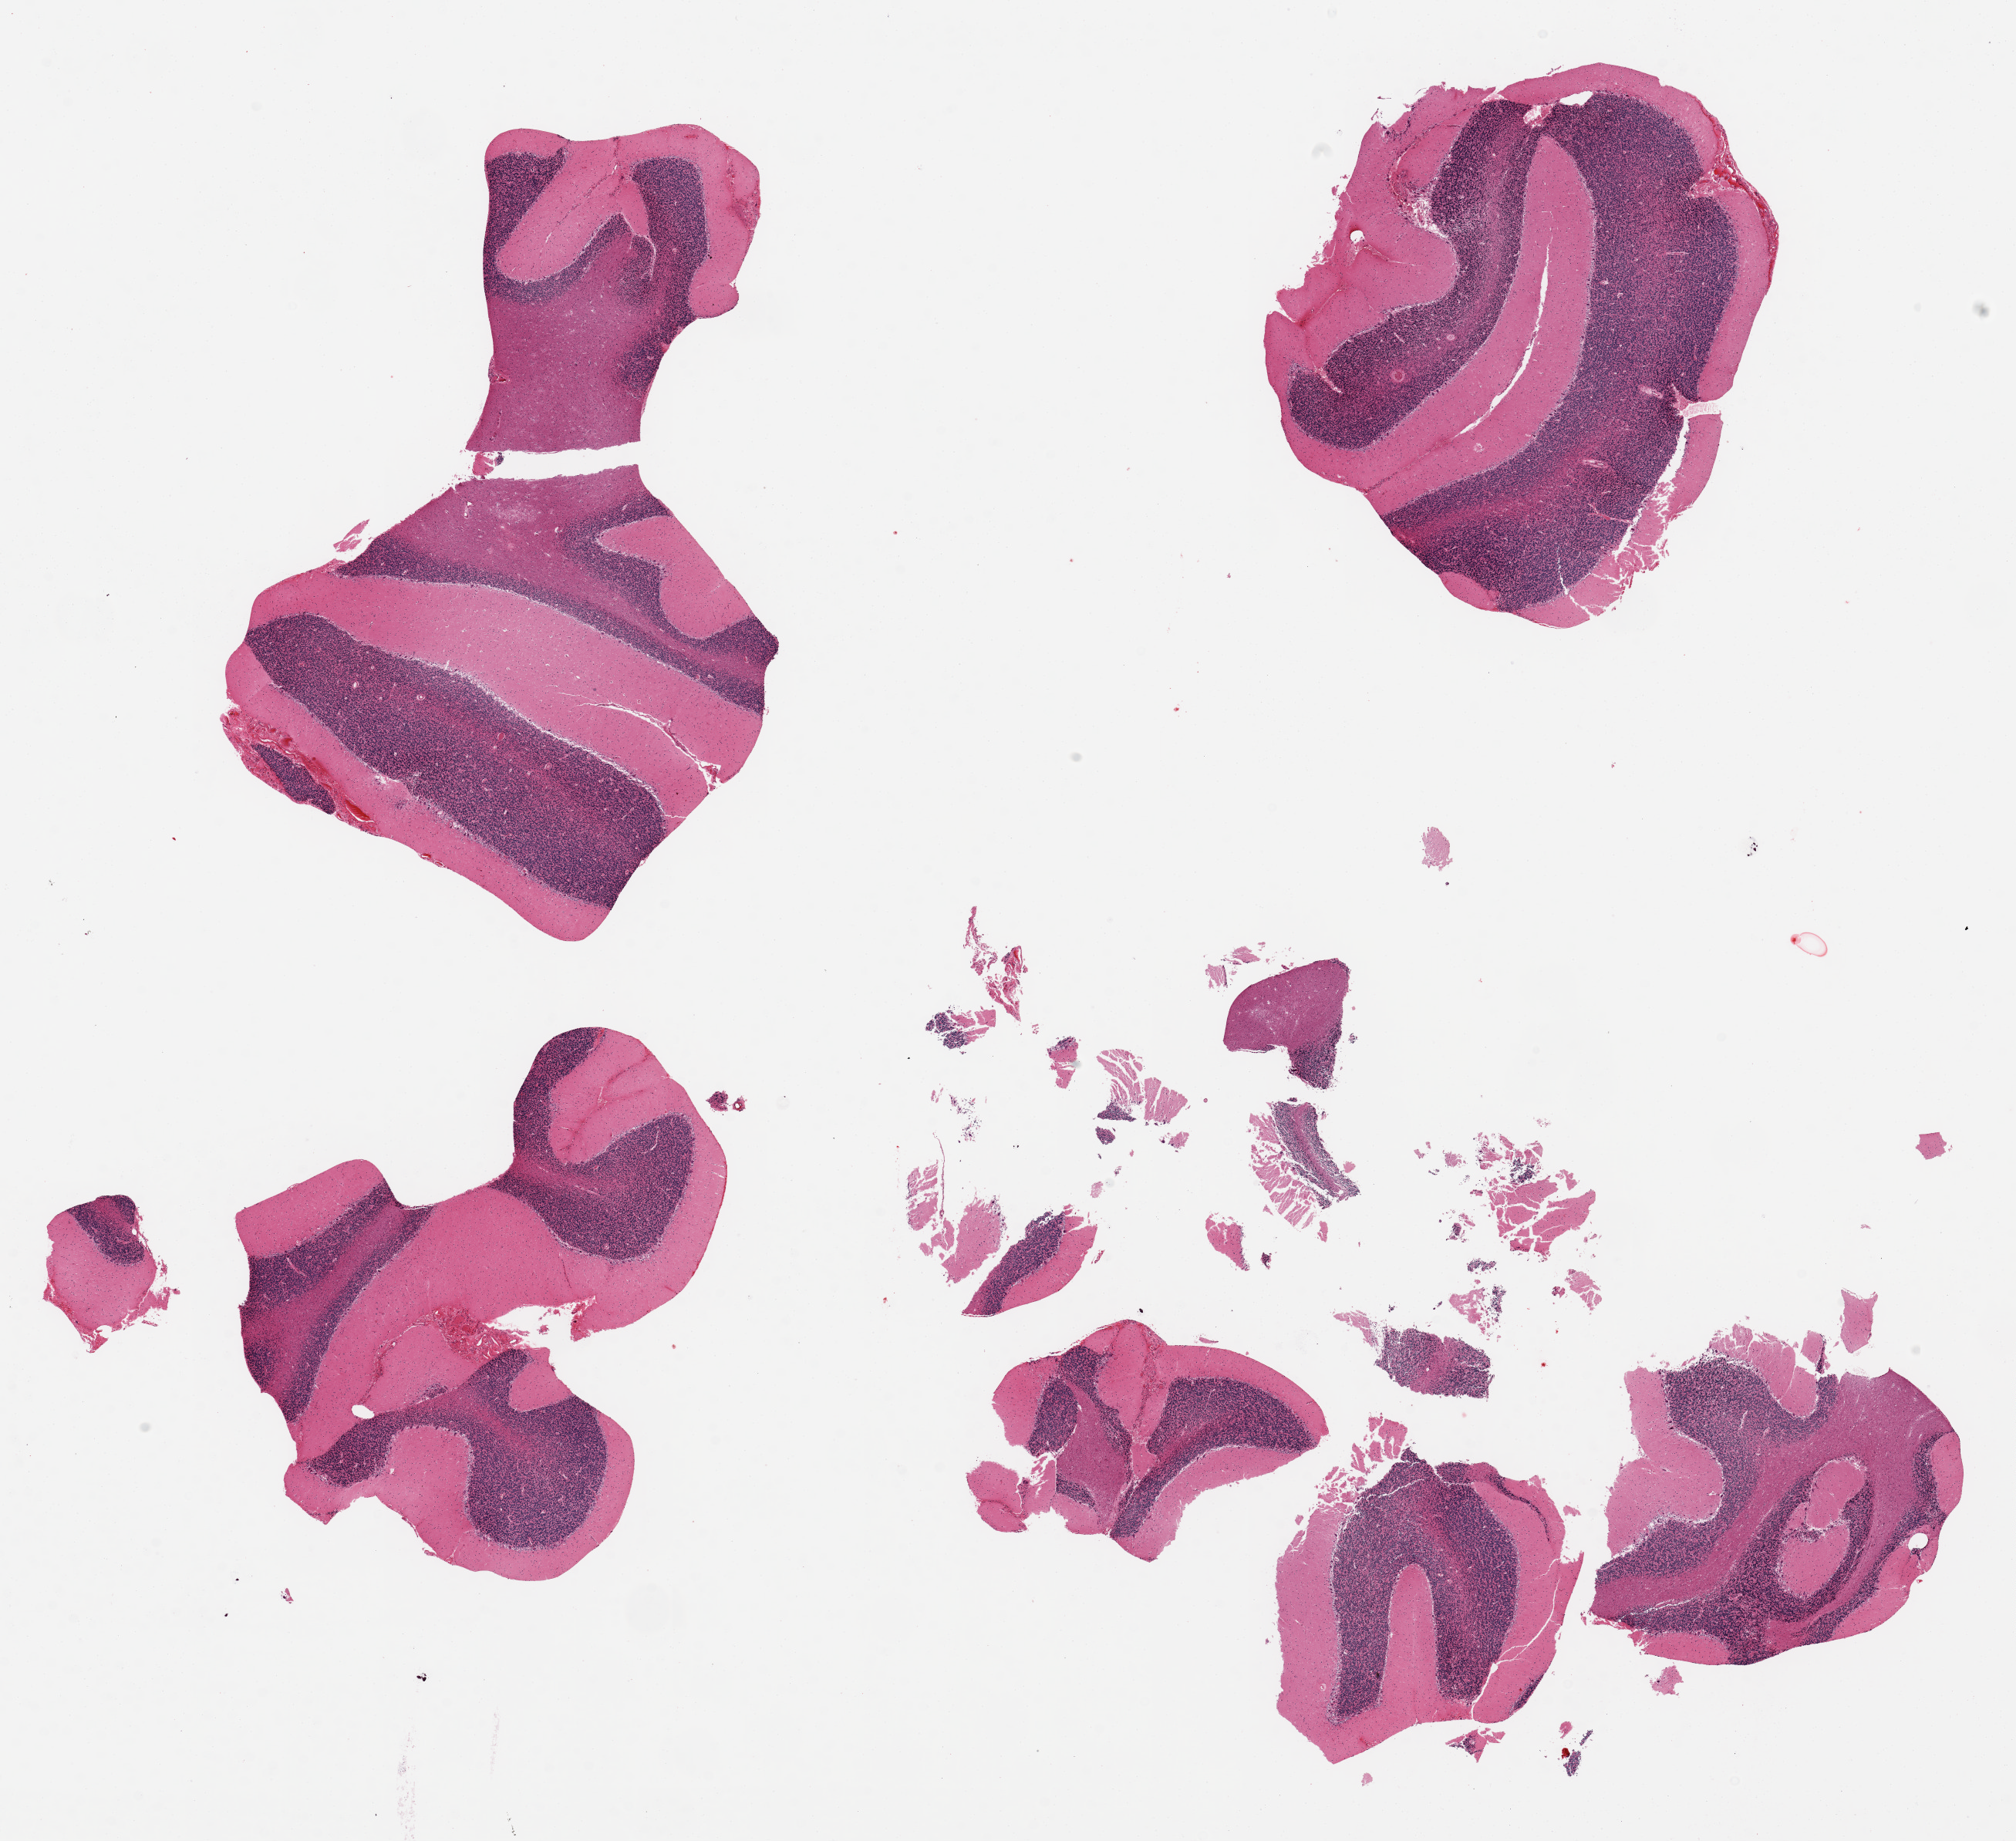
Digitized hematoxylin and eosin (H&E)-stained section — whole scanned area (about 20.7 x 18.9 mm) shown as a low-resolution overview; PAXgene-fixed, paraffin-embedded tissue; section of cerebellum (target tissue); donor tissue sample. Donor sex: male.
Pathologist's review note for this sample: 4 pieces ~5 mm cubed, 1 piece fragmented.